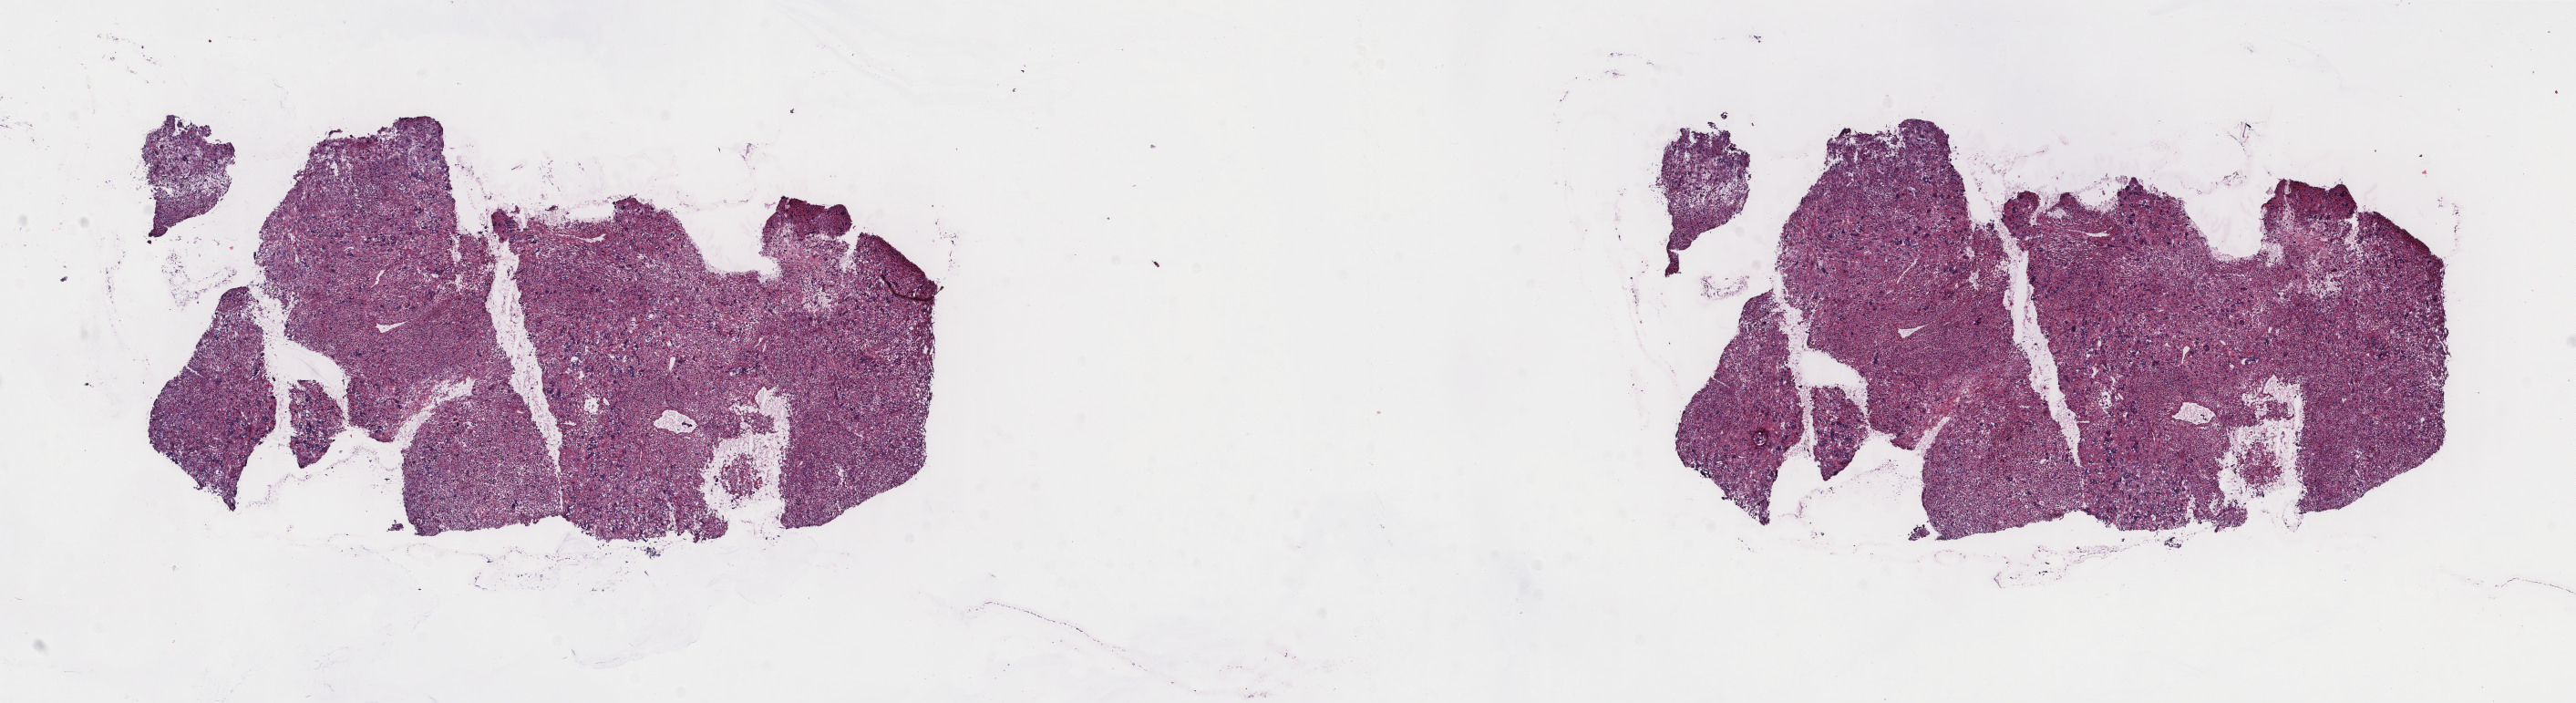
Whole-slide histology image, Hematoxylin and eosin (H&E) stained — a low-resolution overview of the entire scanned area, about 22.4 x 6.1 mm, frozen section from the top of the tissue portion, sample: primary tumour, connective, subcutaneous and other soft tissues. Female patient; age at initial diagnosis 67 years. Composition of this section per pathologist review: tumour cells 100%, tumour nuclei 97%, normal cells 0%, stromal cells 0%, necrosis 0%. Inflammatory infiltration, as recorded: lymphocyte infiltration 0%, monocyte infiltration 0%, neutrophil infiltration 0%.
- histologic diagnosis: Leiomyosarcoma, NOS (connective, subcutaneous and other soft tissues of lower limb and hip)